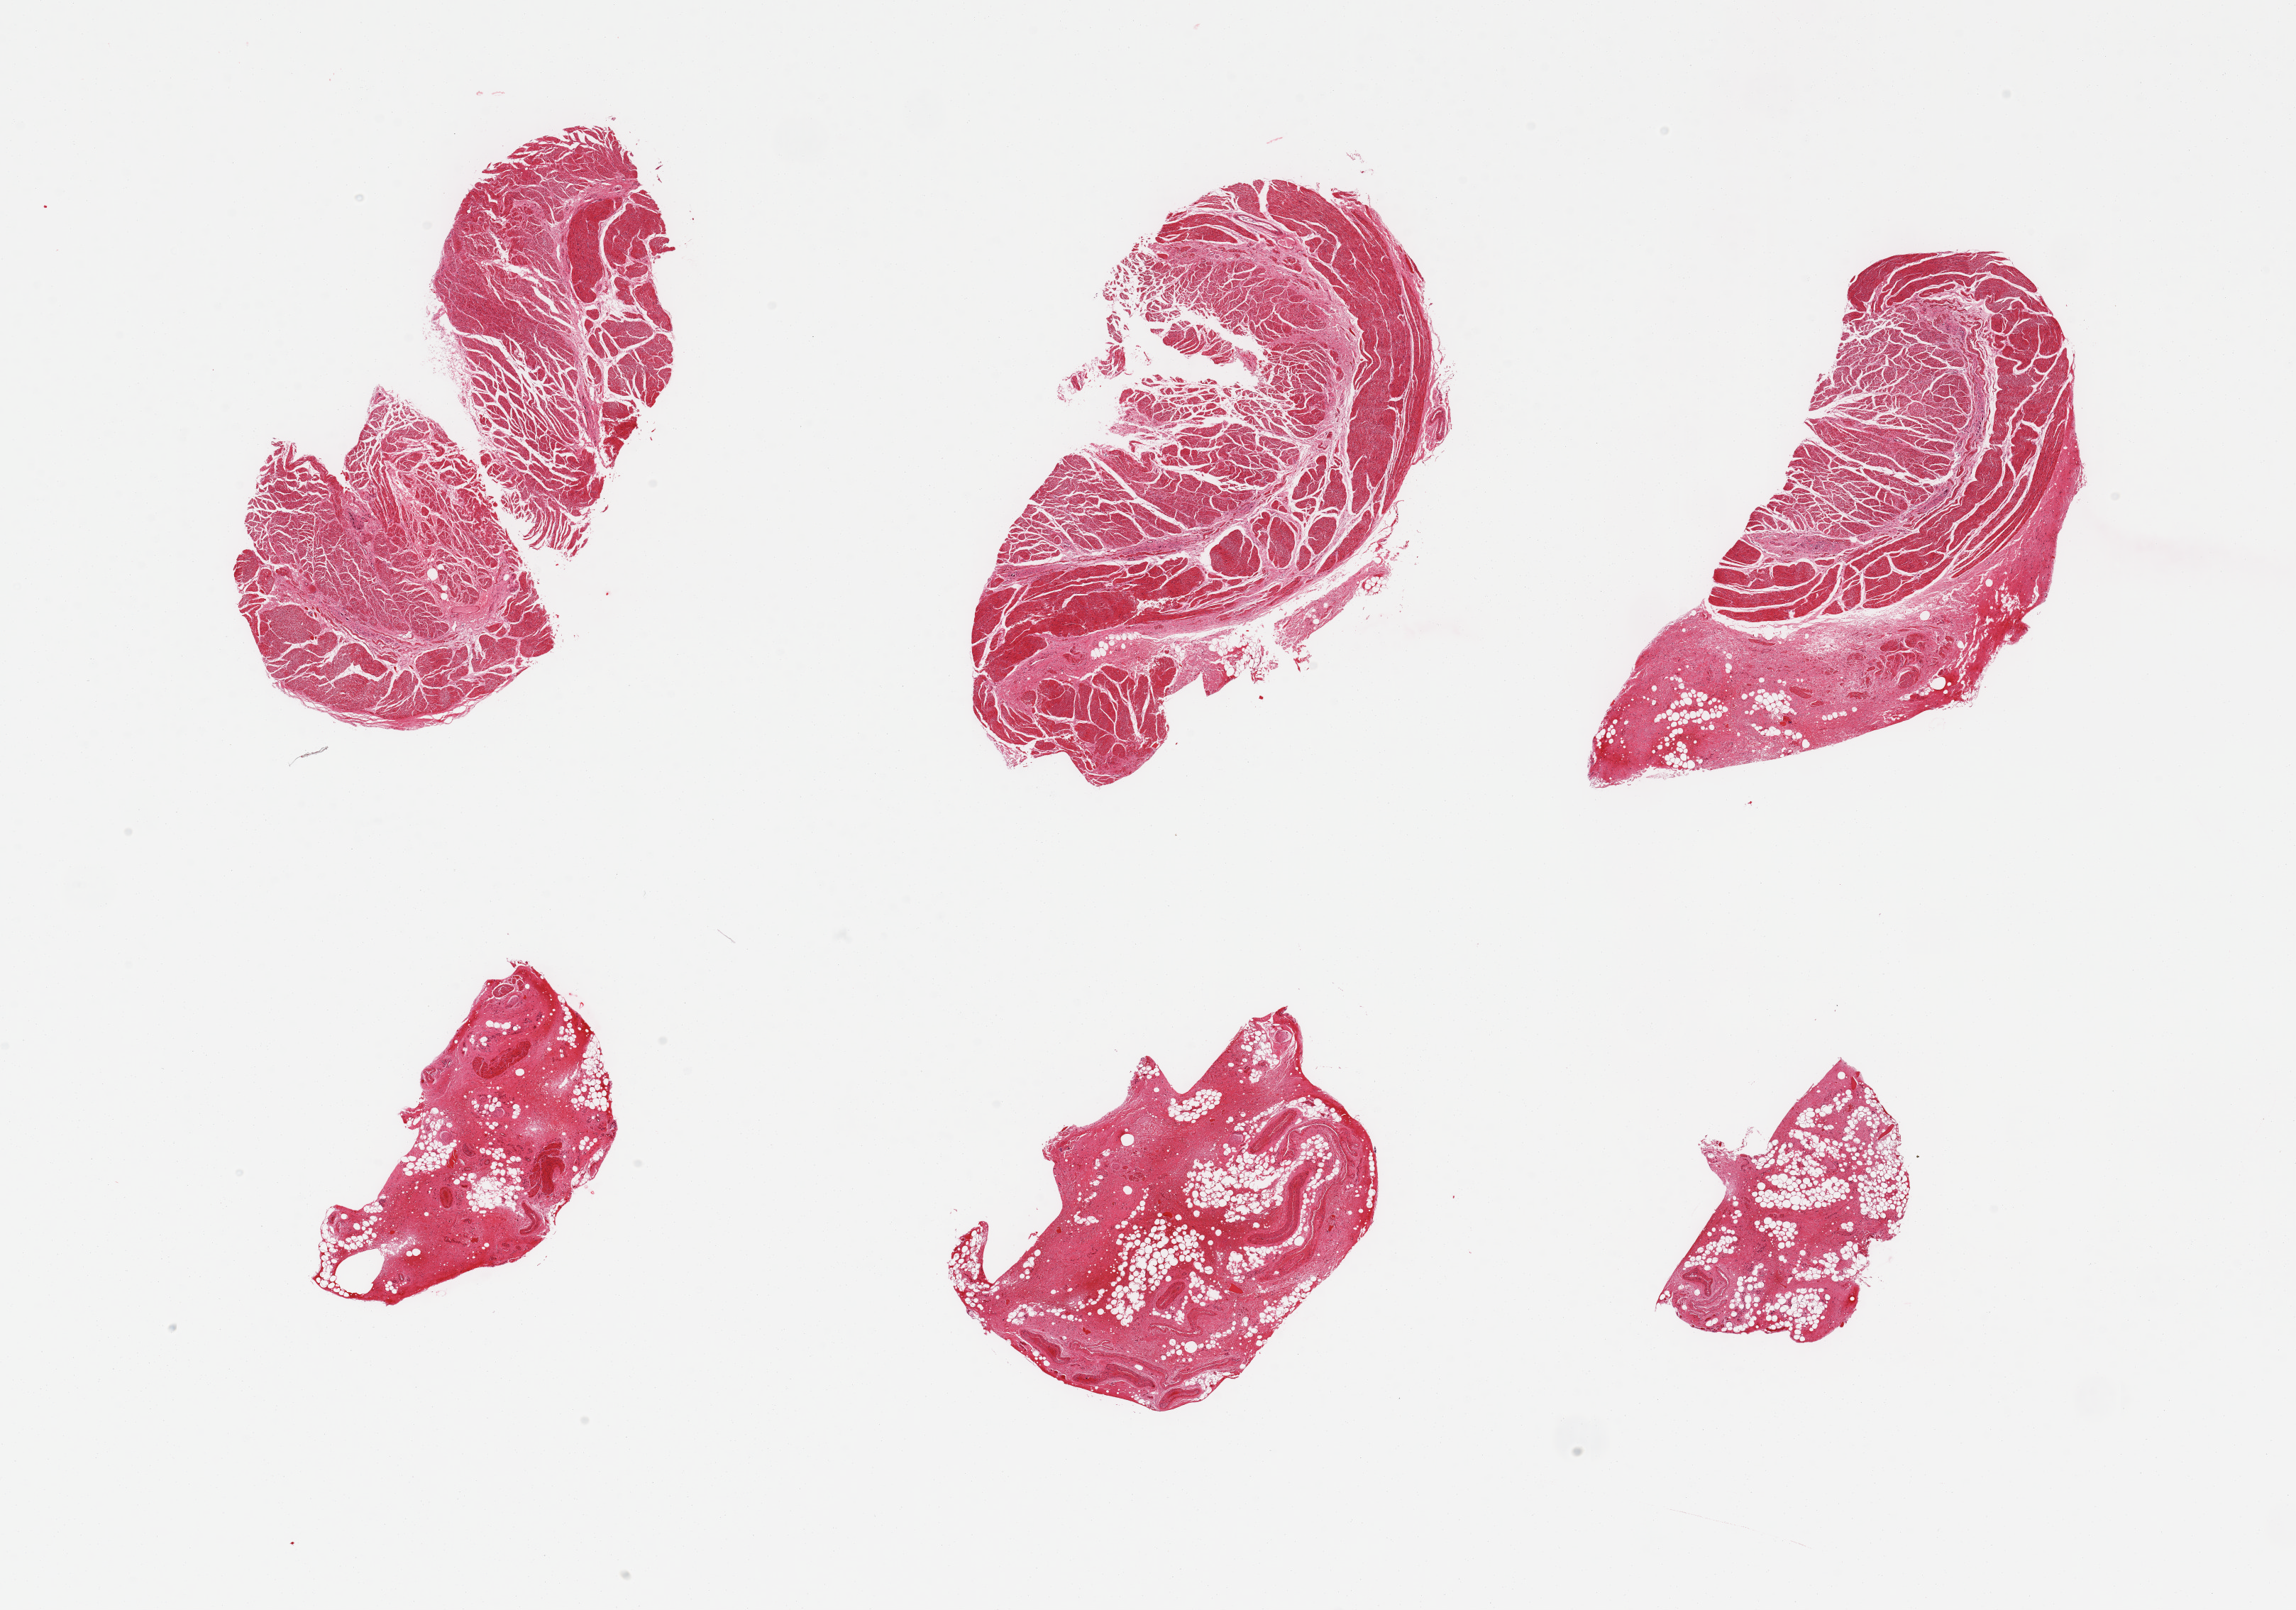
Haematoxylin and eosin whole-slide image — low-resolution overview of the scanned area, about 25.6 x 17.9 mm; PAXgene-fixed, paraffin-embedded tissue; sampled site (target tissue): esophageal muscle; tissue donor sample.
Reviewer comment on this tissue sample: 6 pieces, confirmed target muscularis.